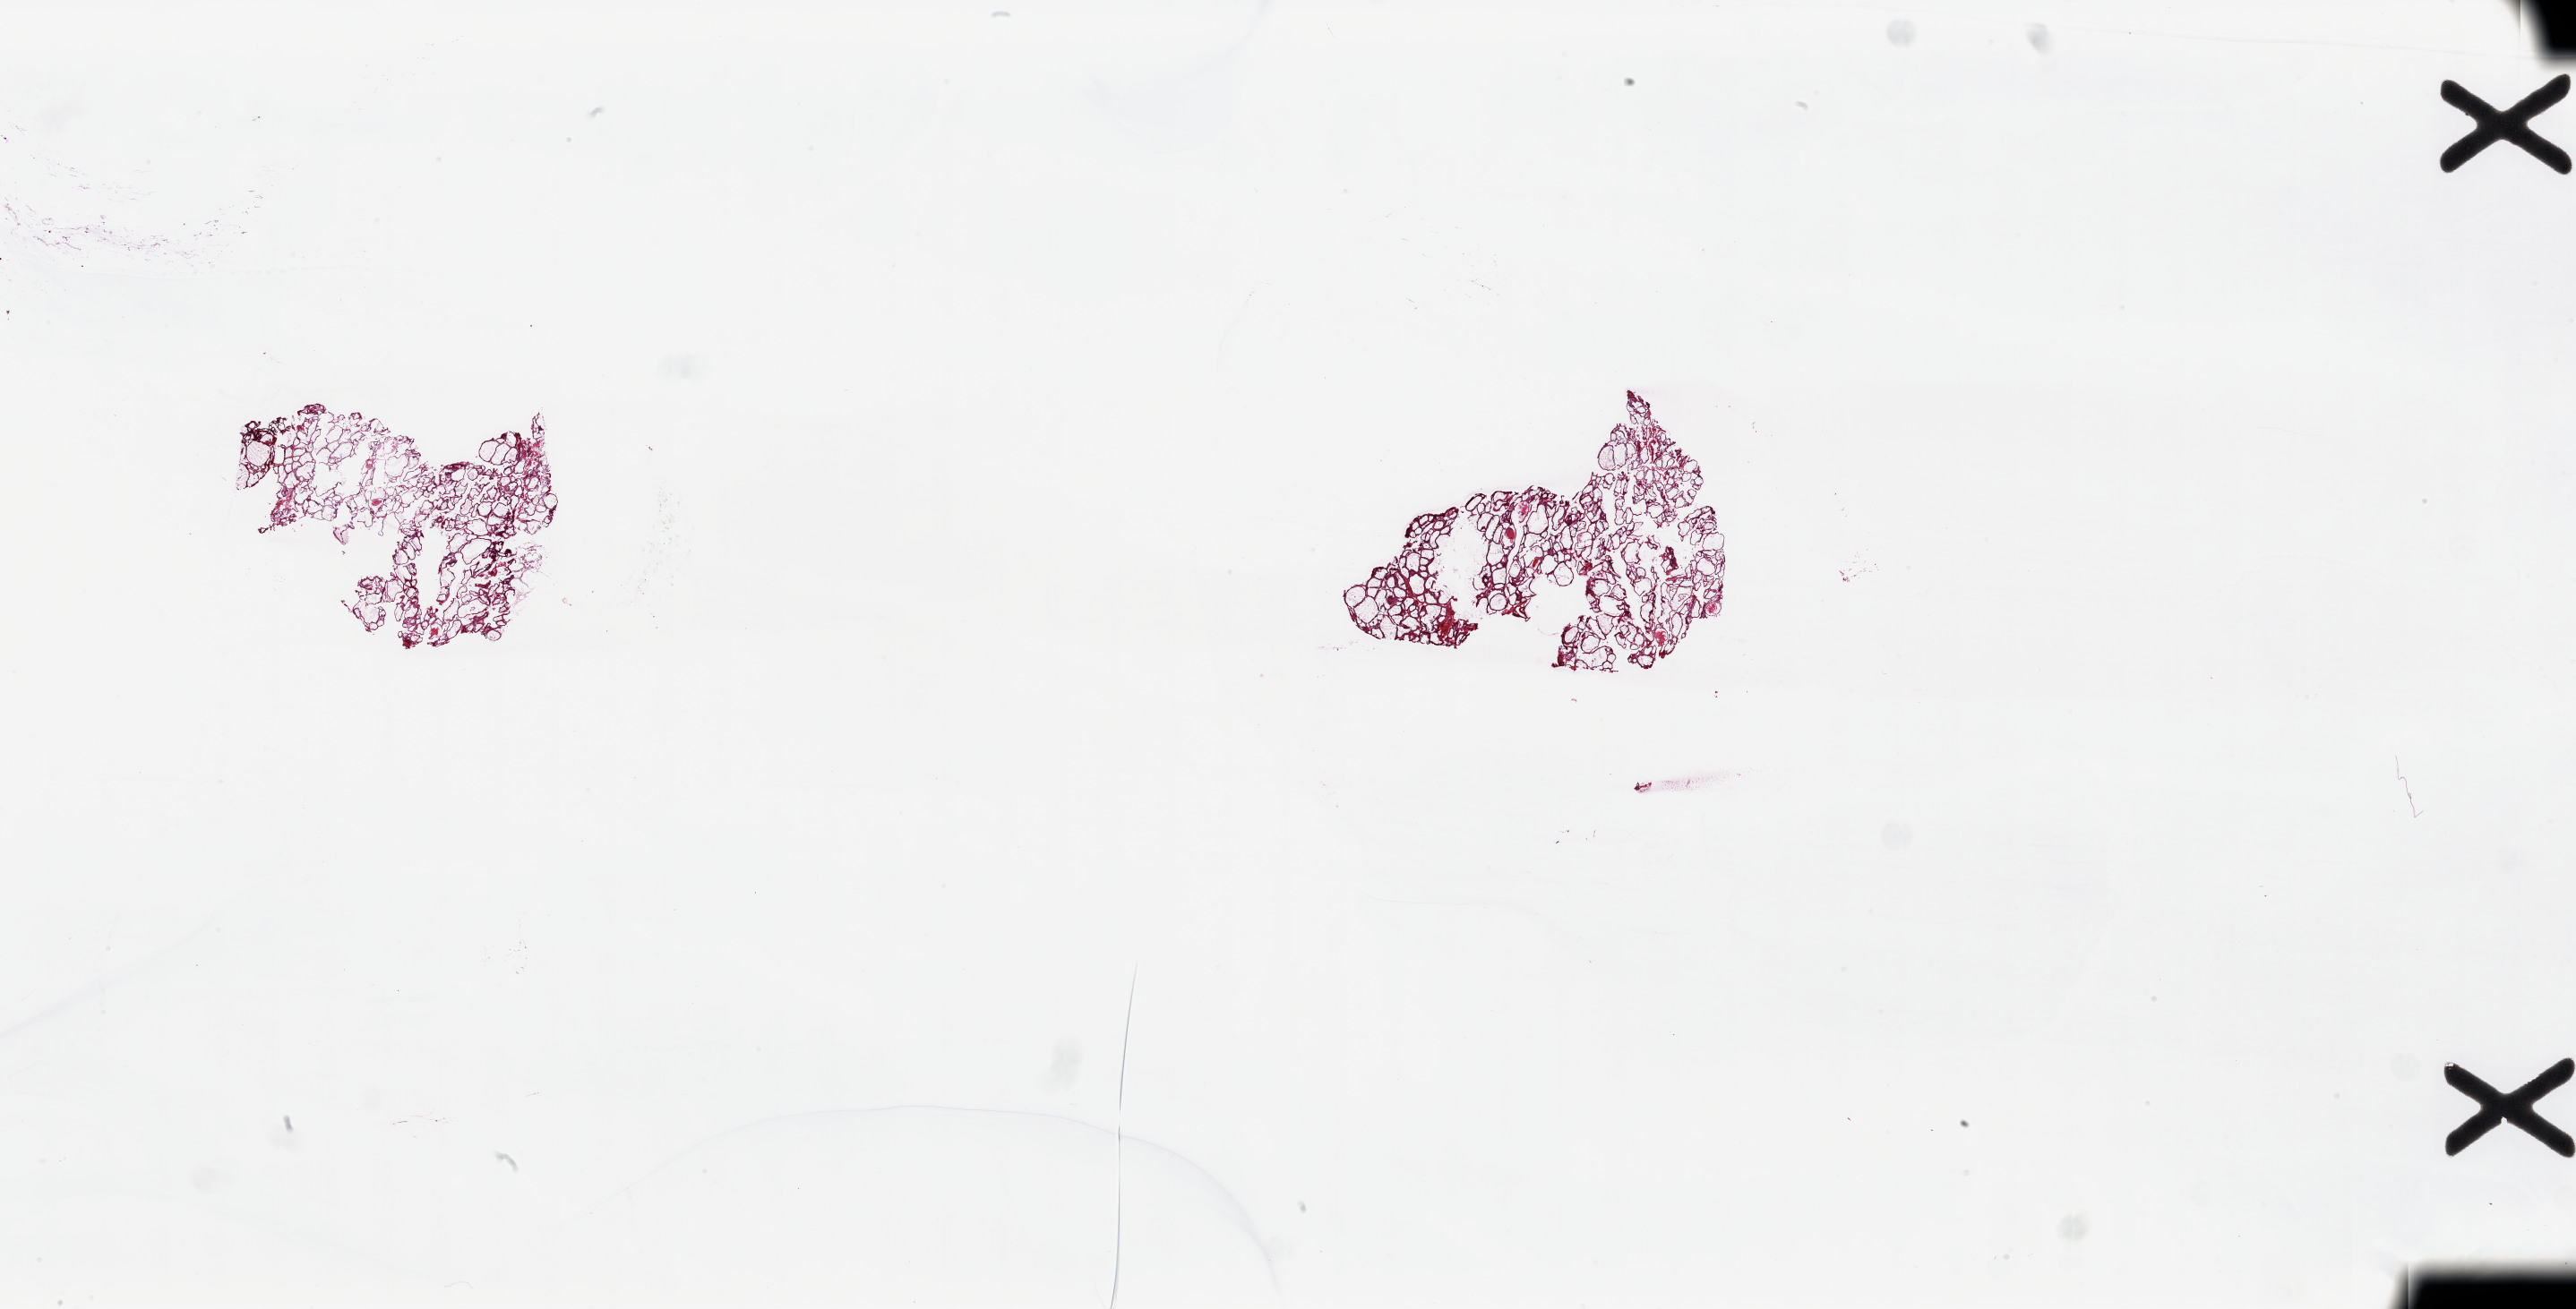
Whole-slide histology image, H&E, a low-resolution overview of the entire scanned area, about 45.6 x 23.2 mm (from a 20x scan). Frozen section from the top of the tissue portion. Sample: solid tissue normal (non-tumour tissue), thyroid. Patient: male, age at initial diagnosis 31 years. Composition of this section per pathologist review: tumour cells 0%, tumour nuclei 0%, normal cells 100%, stromal cells 0%, necrosis 0%. Inflammatory infiltration, as recorded: lymphocyte infiltration 0%, monocyte infiltration 0%, neutrophil infiltration 0%.
* this section: solid tissue normal sample (biorepository sample class)
* patient diagnosis: Papillary adenocarcinoma, NOS